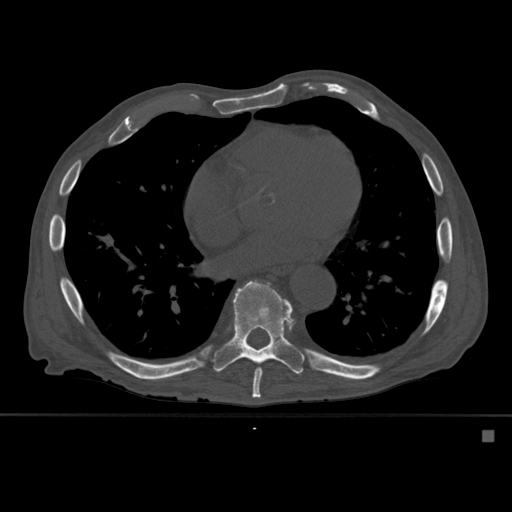
CT including the spine, one axial slice; position 337 of 527 along the scan axis; bone window (W 1800 / L 400 HU); 1.5 mm slice thickness; 512 × 512 image matrix, field of view 373 × 373 mm. Male patient, age 78 years. Case-level facts recorded for this patient, not image findings: primary cancer: prostate.
Annotated regions visible in this slice (semi-automatically segmented with operator editing):
- T8 vertebra: bounding box <252,368,262,398> (left, top, right, bottom; pixels)
- T9 vertebra: <213,280,305,386>